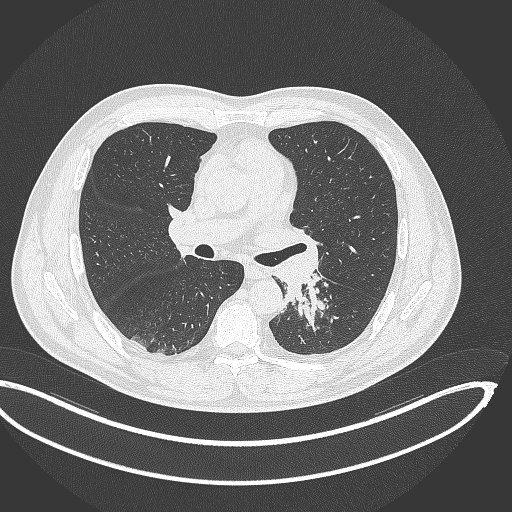
Chest CT, one axial slice; position 203 of 362 along the scan axis; lung window (W 1500 / L -600 HU); 1 mm slice thickness; 512 × 512 image matrix, field of view 442 × 442 mm. Male patient, age 50 years. From the clinical record (not read from this slice): clinical TNM (as recorded): T2a N3 M0.
Structures marked on this image (rectangle marked by the reading radiologist):
- lung tumour (recorded histology: squamous cell carcinoma): bounding box (x1, y1, x2, y2) in pixels: (284, 270, 322, 331)